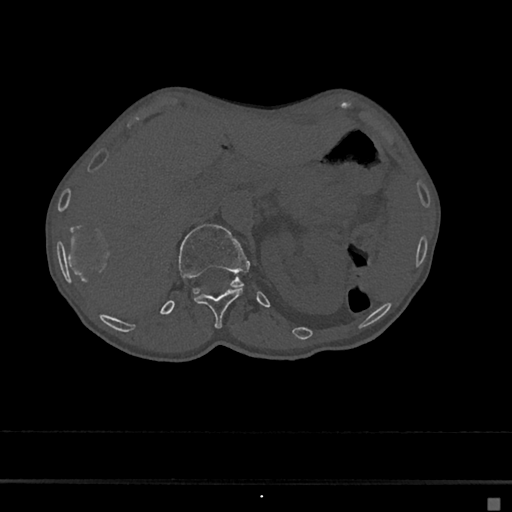
CT including the spine, one axial slice. Bone window (W 1800 / L 400 HU). 0.5 mm slice thickness. 512 × 512 image matrix, field of view 360 × 360 mm. Patient: female, 68 years. From the clinical record (not read from this slice): primary cancer: renal.
Outlined on this slice (semi-automatically segmented with operator editing):
- L1 vertebra: box from (x=177, y=224) to (x=251, y=293) px
- T12 vertebra: (x=195, y=289)–(x=243, y=329)